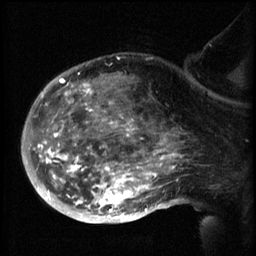
Breast MRI (dynamic contrast-enhanced), one sagittal slice; slice 41 of 60 in the series (ordered by position); 3 images stored at this slice position (order not interpretable as contrast timing); 1.5 T; TE 4.2 ms, TR 8.2 ms; 2.3 mm slice thickness; 256 × 256 image matrix. Patient: female, 50 years.
Annotated regions visible in this slice (semi-automatic segmentation, software-assisted and operator-edited):
- analysis volume of interest (the breast-tissue region the enhancement analysis was run in; not a lesion): bounding box (x1, y1, x2, y2) in pixels: (50, 64, 169, 217)
- tumour enhancement mask (voxels above the 70 % enhancement threshold inside the analysis volume of interest): (50, 76, 169, 217)